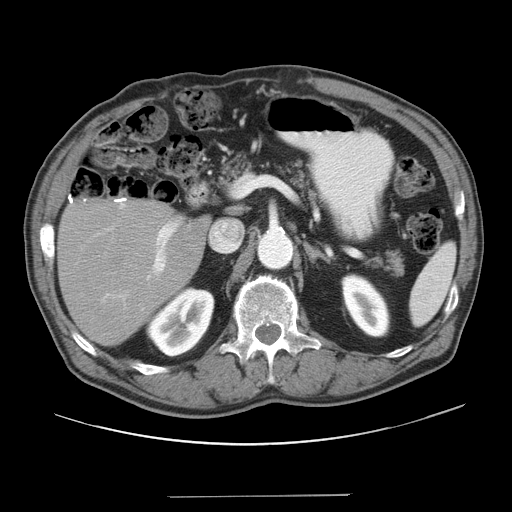
Contrast-enhanced abdominal CT, one axial slice. 120 kVp. Intravenous contrast given. Soft-tissue window (W 400 / L 40 HU). 512 × 512 image matrix, field of view 420 × 420 mm. Male patient, age 75 years. Case-level facts recorded for this patient, not image findings: diagnosis: colorectal cancer liver metastases, imaged before liver resection; multiple liver metastases: no.
Structures marked on this image (expert manual segmentation):
- liver: bounding box (x1, y1, x2, y2) in pixels: (59, 200, 208, 345)
- planned liver remnant (the part of the liver to remain after resection): (60, 201, 207, 346)
- portal vein (with intrahepatic branches): (102, 200, 180, 308)